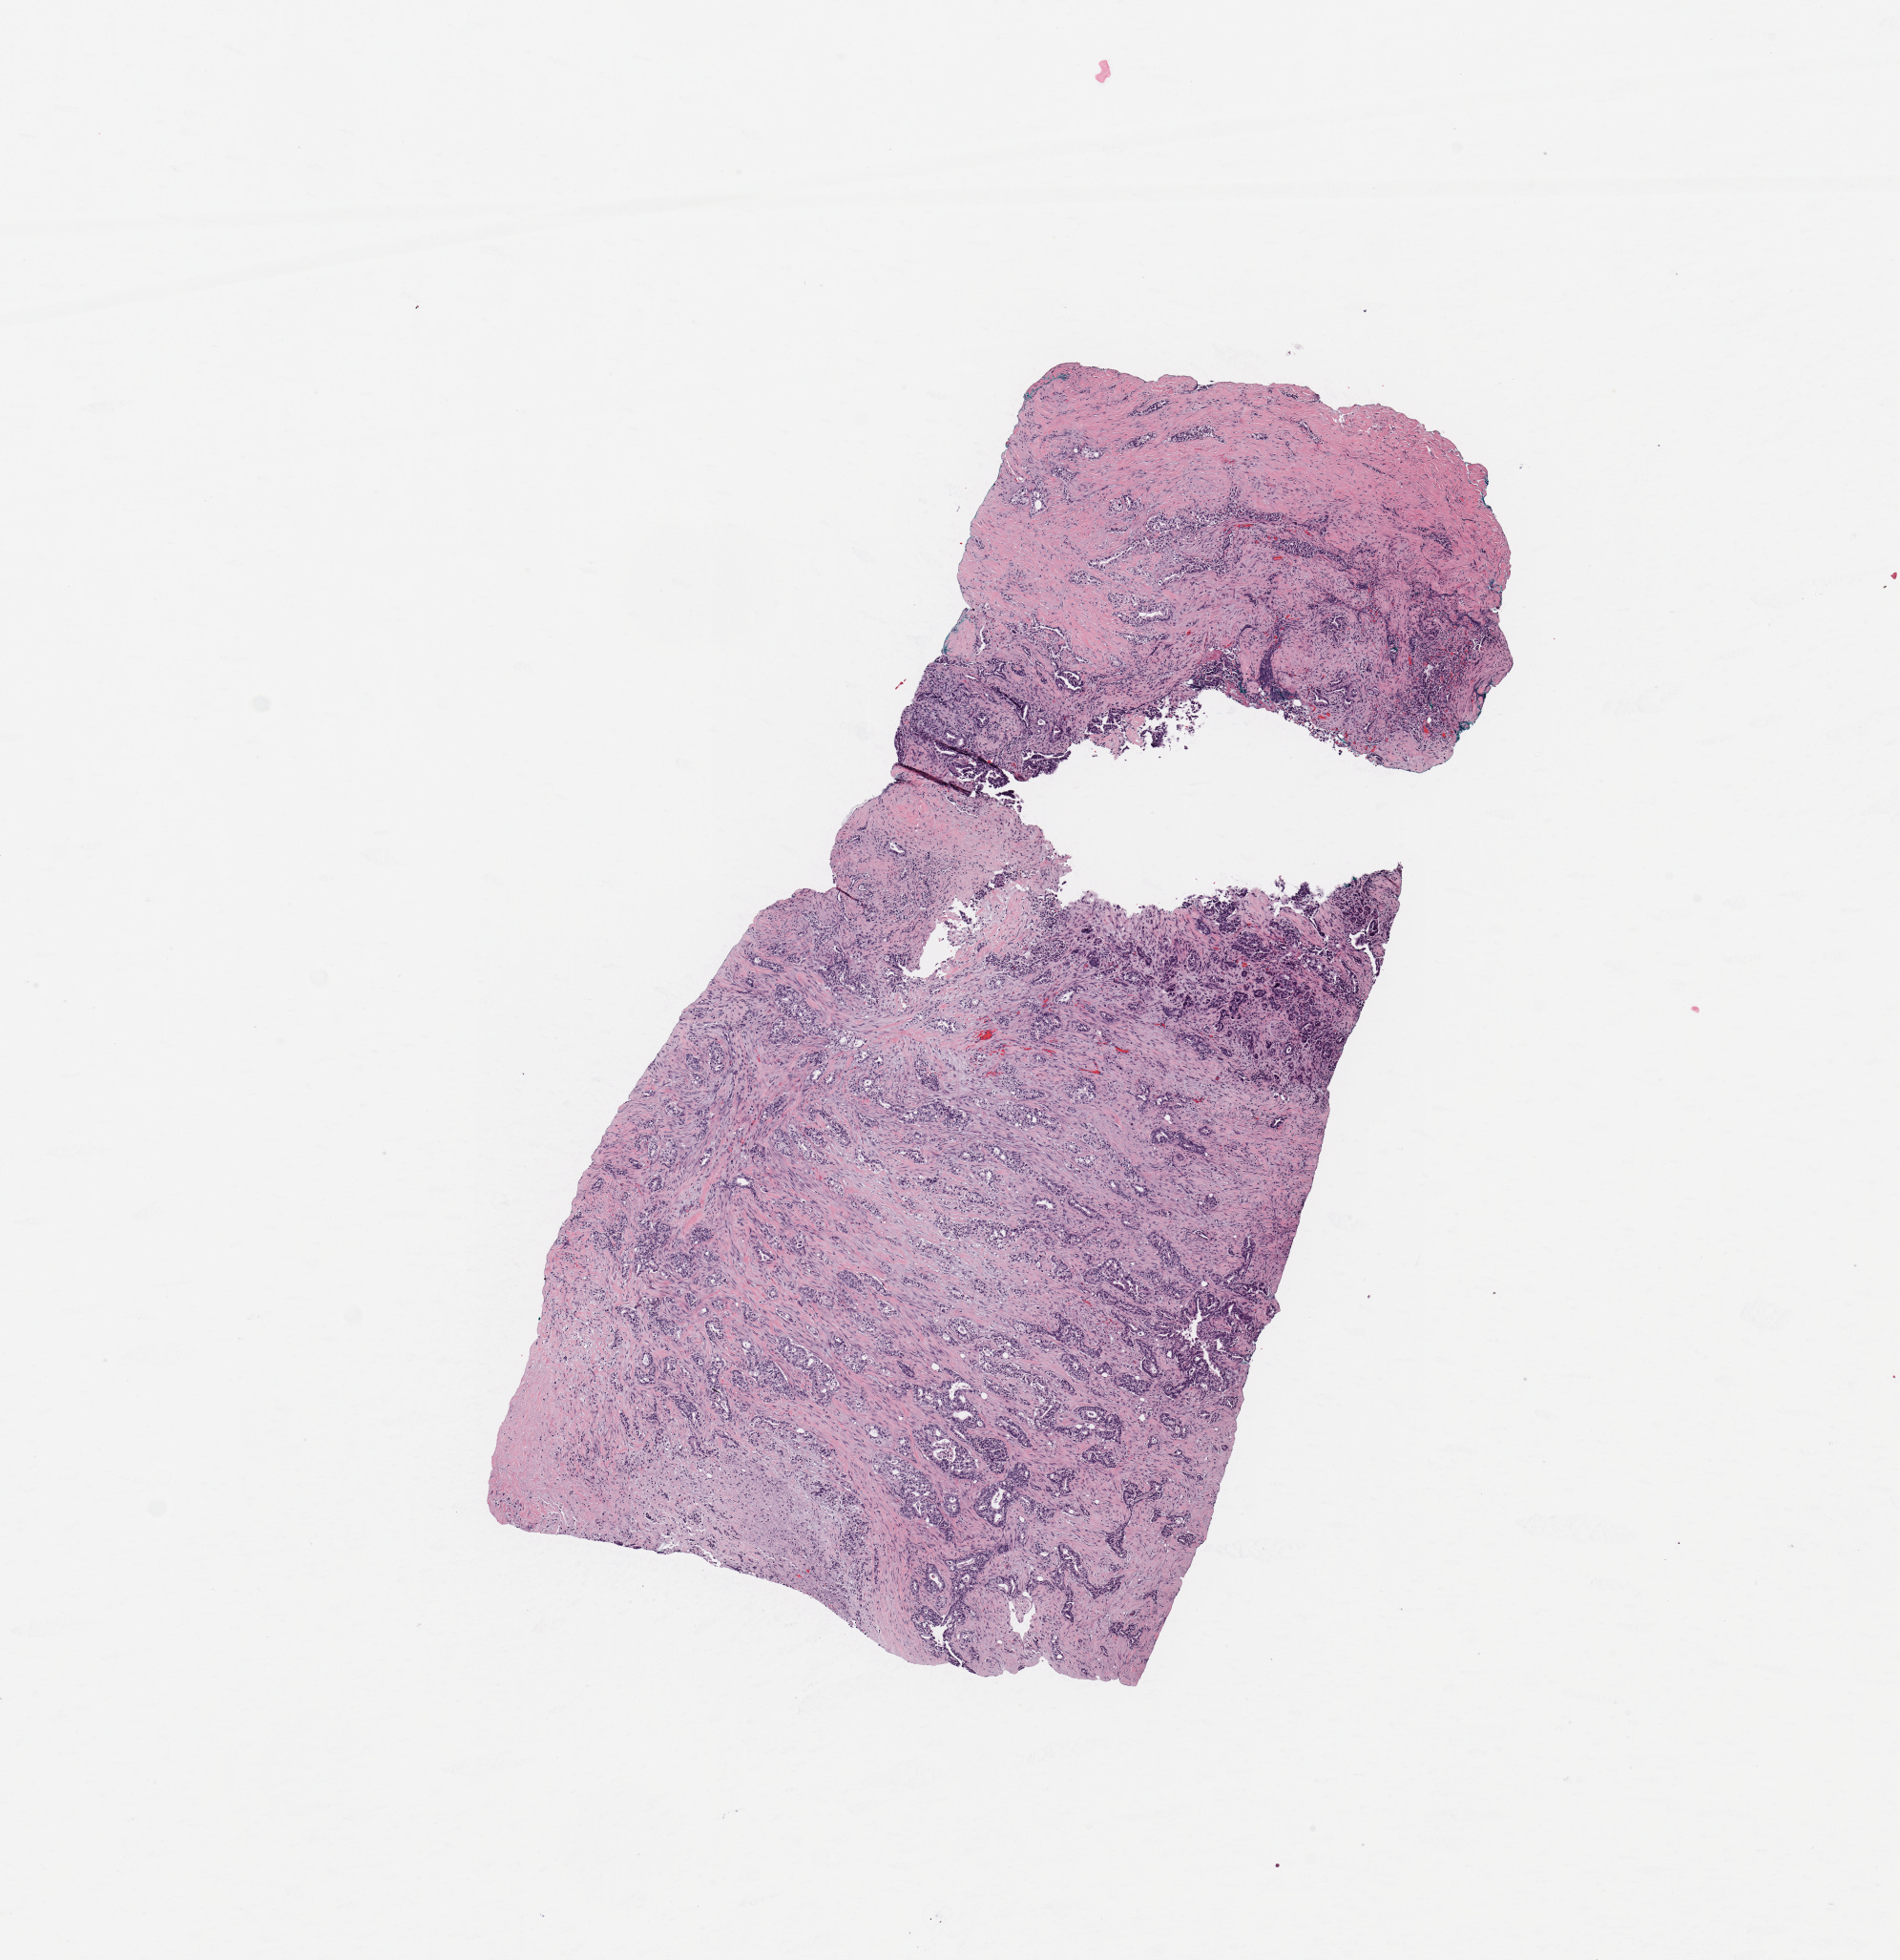
Hematoxylin and eosin (H&E) stained whole-slide image — a low-resolution overview of the entire scanned area, about 7.9 x 8.1 mm; tumour tissue sample, sampled site: pancreas. Patient: male, age 70 years. Histologic grade: G3 (poorly differentiated). Pathologist review of this section (percent, as recorded): tumour nuclei 50%, necrosis 0%.
Primary tumour site (as recorded): head. AJCC pathologic stage: IIB. Histologic diagnosis: Infiltrating duct carcinoma, NOS.